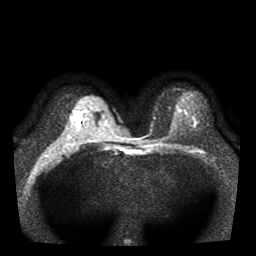
Breast MRI, one axial slice. Slice 21 of 41 in the series (ordered by position). Diffusion-weighted series; image 2 of 4 stored at this slice position (different b-values; order by instance number). 1.5 T. 5 mm slice thickness. 256 × 256 image matrix, field of view 330 × 330 mm. Female patient.
Outlined on this slice (expert manual segmentation):
- tumour on diffusion-weighted imaging: box from (x=77, y=113) to (x=83, y=120) px